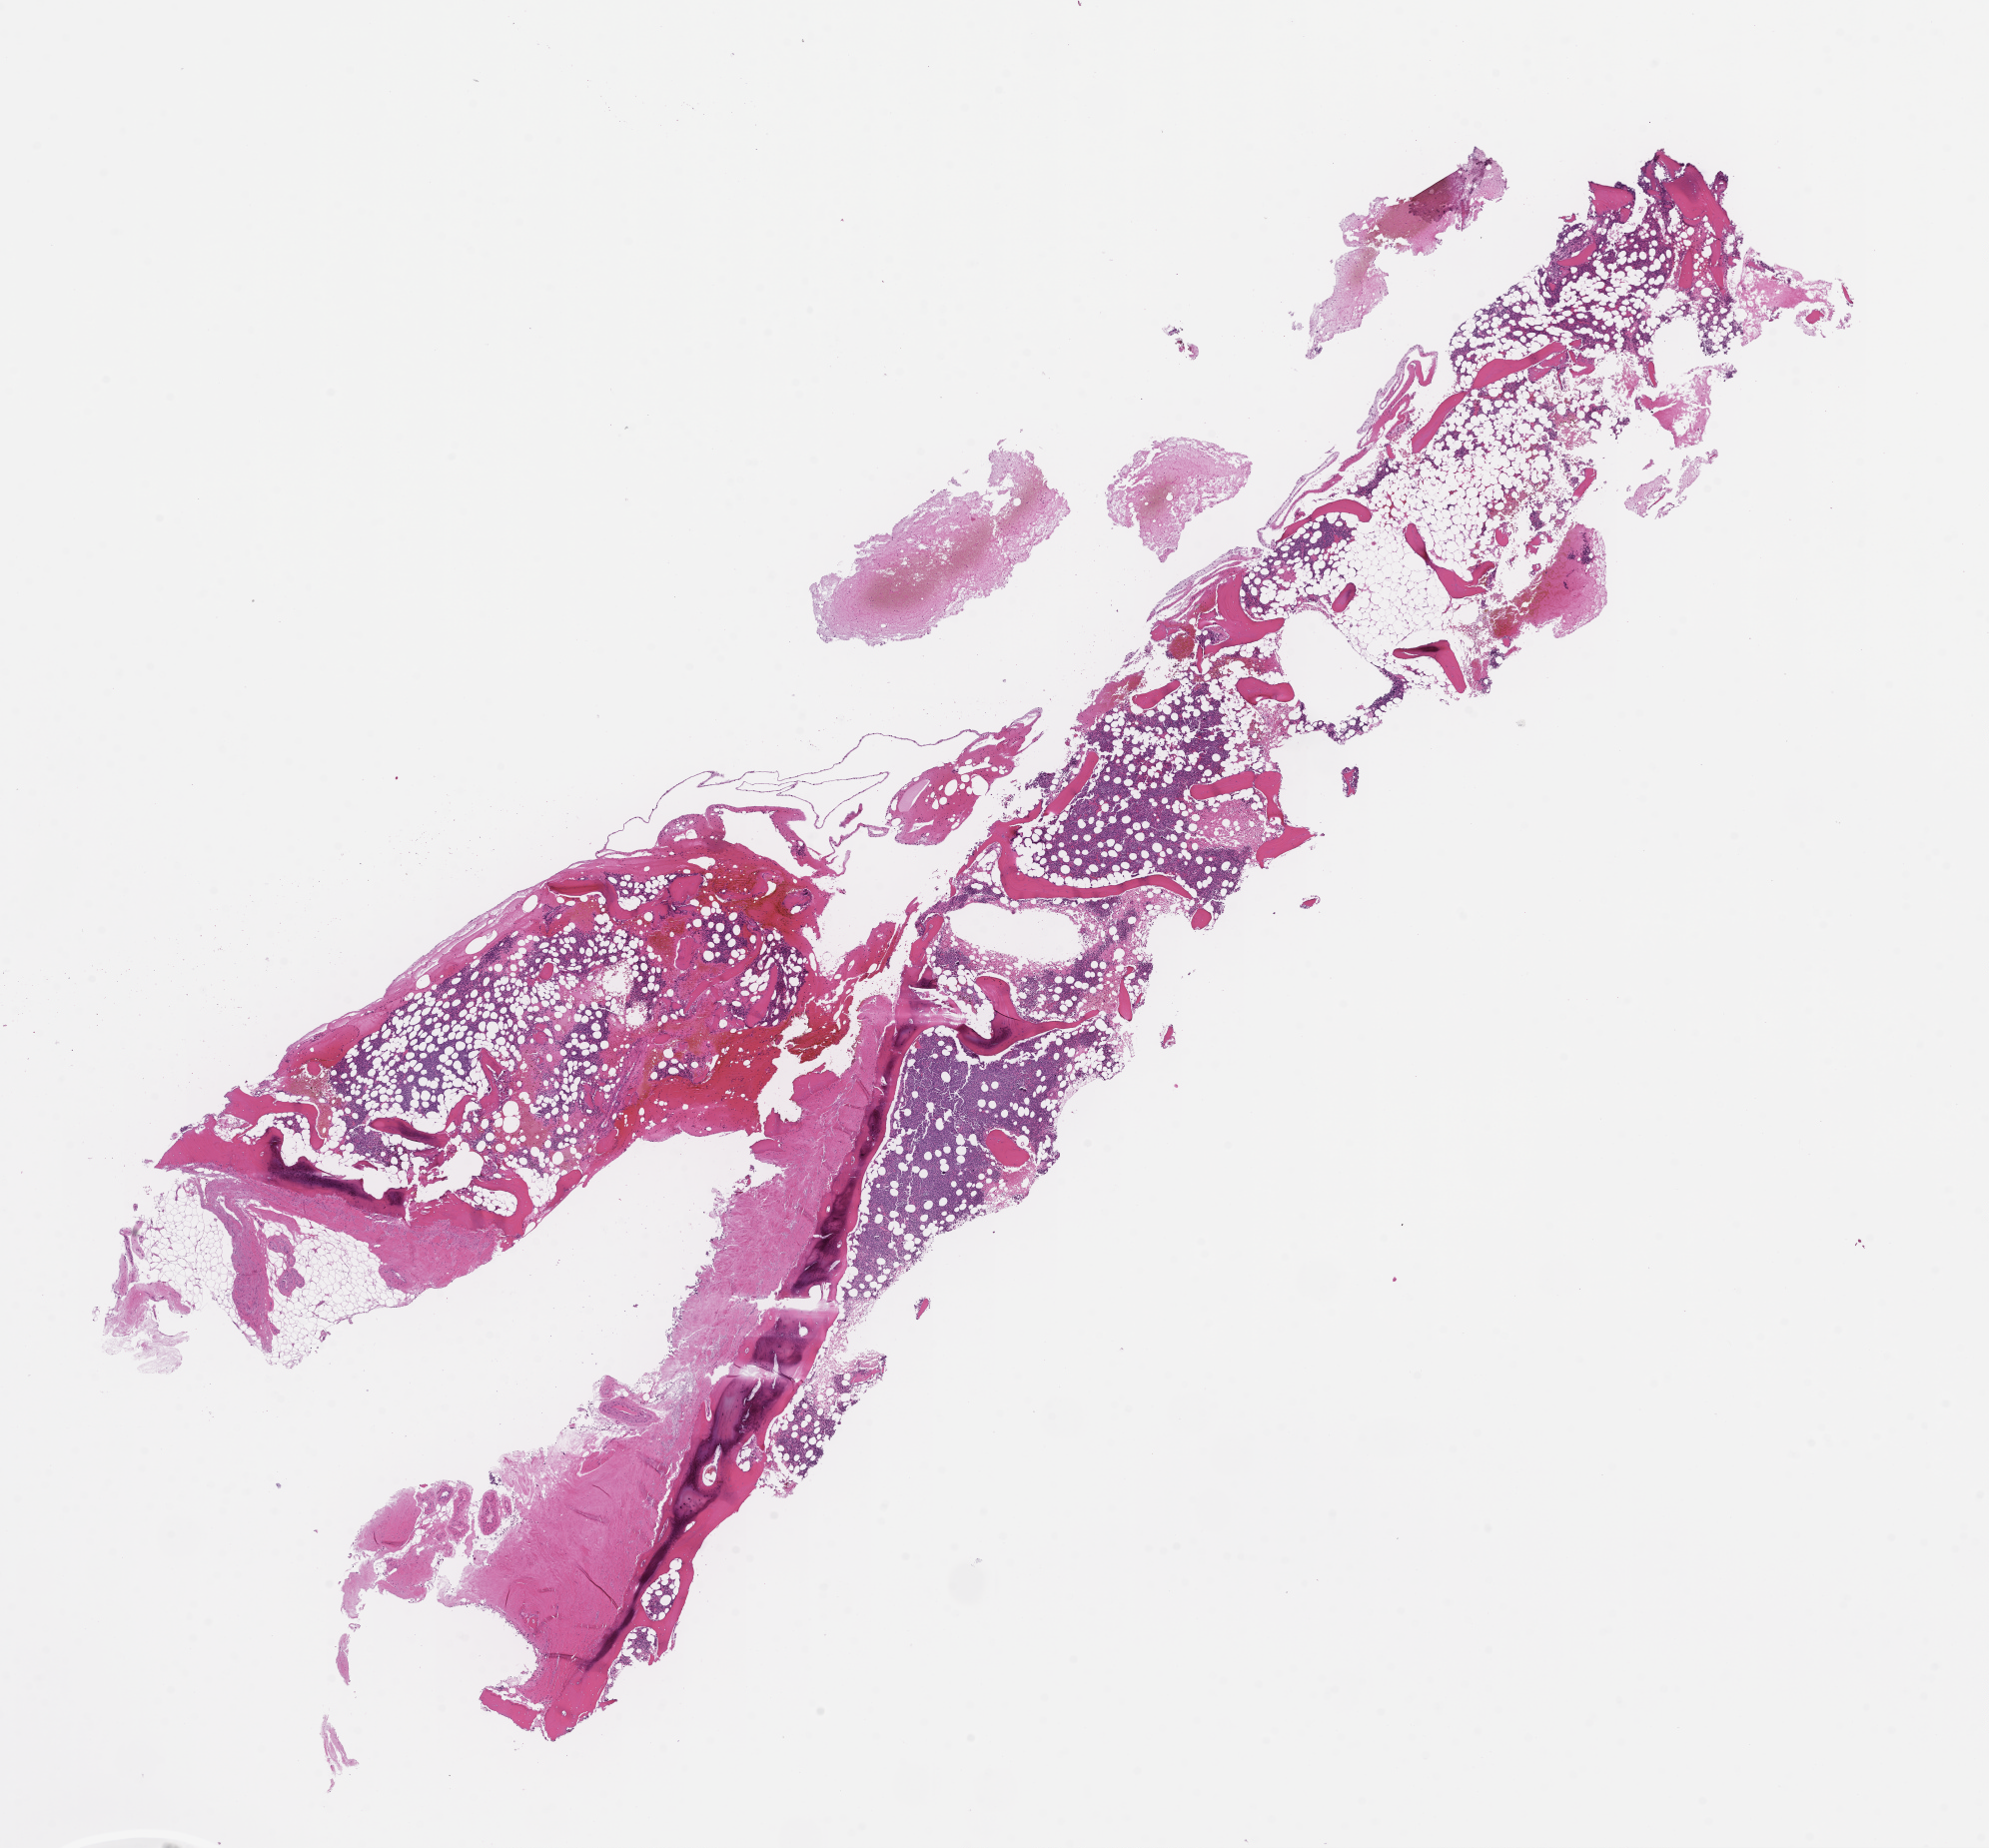
Whole-slide image, hematoxylin and eosin (H&E) stain — whole scanned area (about 16.1 x 14.9 mm) shown as a low-resolution overview, formalin-fixed paraffin-embedded section, site: bone marrow, archival tissue. Patient: female.
• this section: primary tumor
• diagnosis: Plasma Cell Myeloma